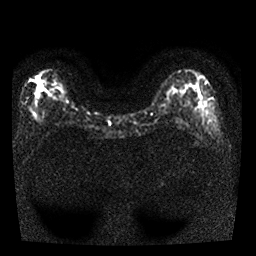
Breast MRI, one axial slice; slice 10 of 25 in the series (ordered by position); diffusion-weighted series; image 2 of 4 stored at this slice position (different b-values; order by instance number); 1.5 T; 4 mm slice thickness; 256 × 256 image matrix, field of view 300 × 300 mm. Female patient.
Structures marked on this image (expert manual segmentation):
- tumour on diffusion-weighted imaging: bounding box [x1, y1, x2, y2] px = [33, 75, 41, 98]